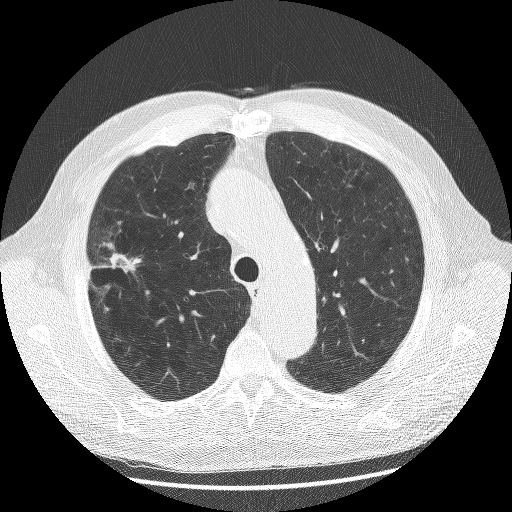
Low-dose screening chest CT, axial slice, first (baseline) screen, lung window (W 1500 / L -600 HU), 2.5 mm slice thickness, lung (sharp) reconstruction kernel (BONE). Male, age 70 years at enrolment.
Lesion marked by an expert reader, bounding box <79,232,147,306> (left, top, right, bottom; pixels). The screening reader recorded 2 non-calcified nodules or masses ≥4 mm on this exam (left upper lobe, right upper lobe); which of them this box marks is not recorded. Official screen result: positive, change unspecified: nodule(s) >= 4 mm or enlarging nodule(s), mass(es), or other non-specific abnormalities suspicious for lung cancer. Participant outcome: lung cancer diagnosed 23 days after this screen — non-small cell carcinoma, right upper lobe, poorly differentiated (G3), stage IA (AJCC 6th edition), 20 mm at pathology.